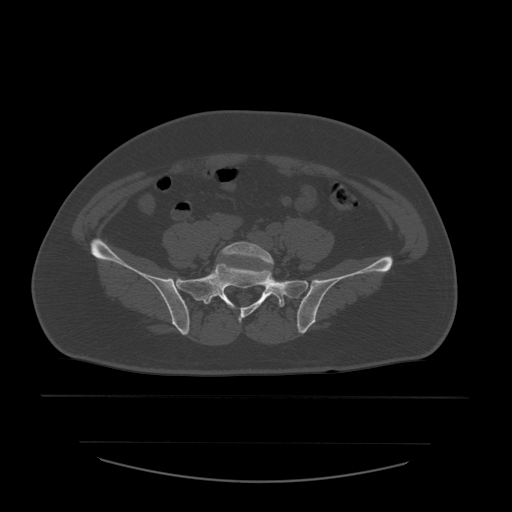
CT including the spine, one axial slice; reconstruction kernel STANDARD; 120 kVp; bone window (W 1800 / L 400 HU); 1.25 mm slice thickness; 512 × 512 image matrix, field of view 441 × 441 mm. Patient age 44 years. Case-level facts recorded for this patient, not image findings: primary cancer: soft tissue sarcoma.
Outlined on this slice (semi-automatic segmentation, software-assisted and operator-edited):
- L5 vertebra: bounding box [x1, y1, x2, y2] px = [213, 242, 285, 306]